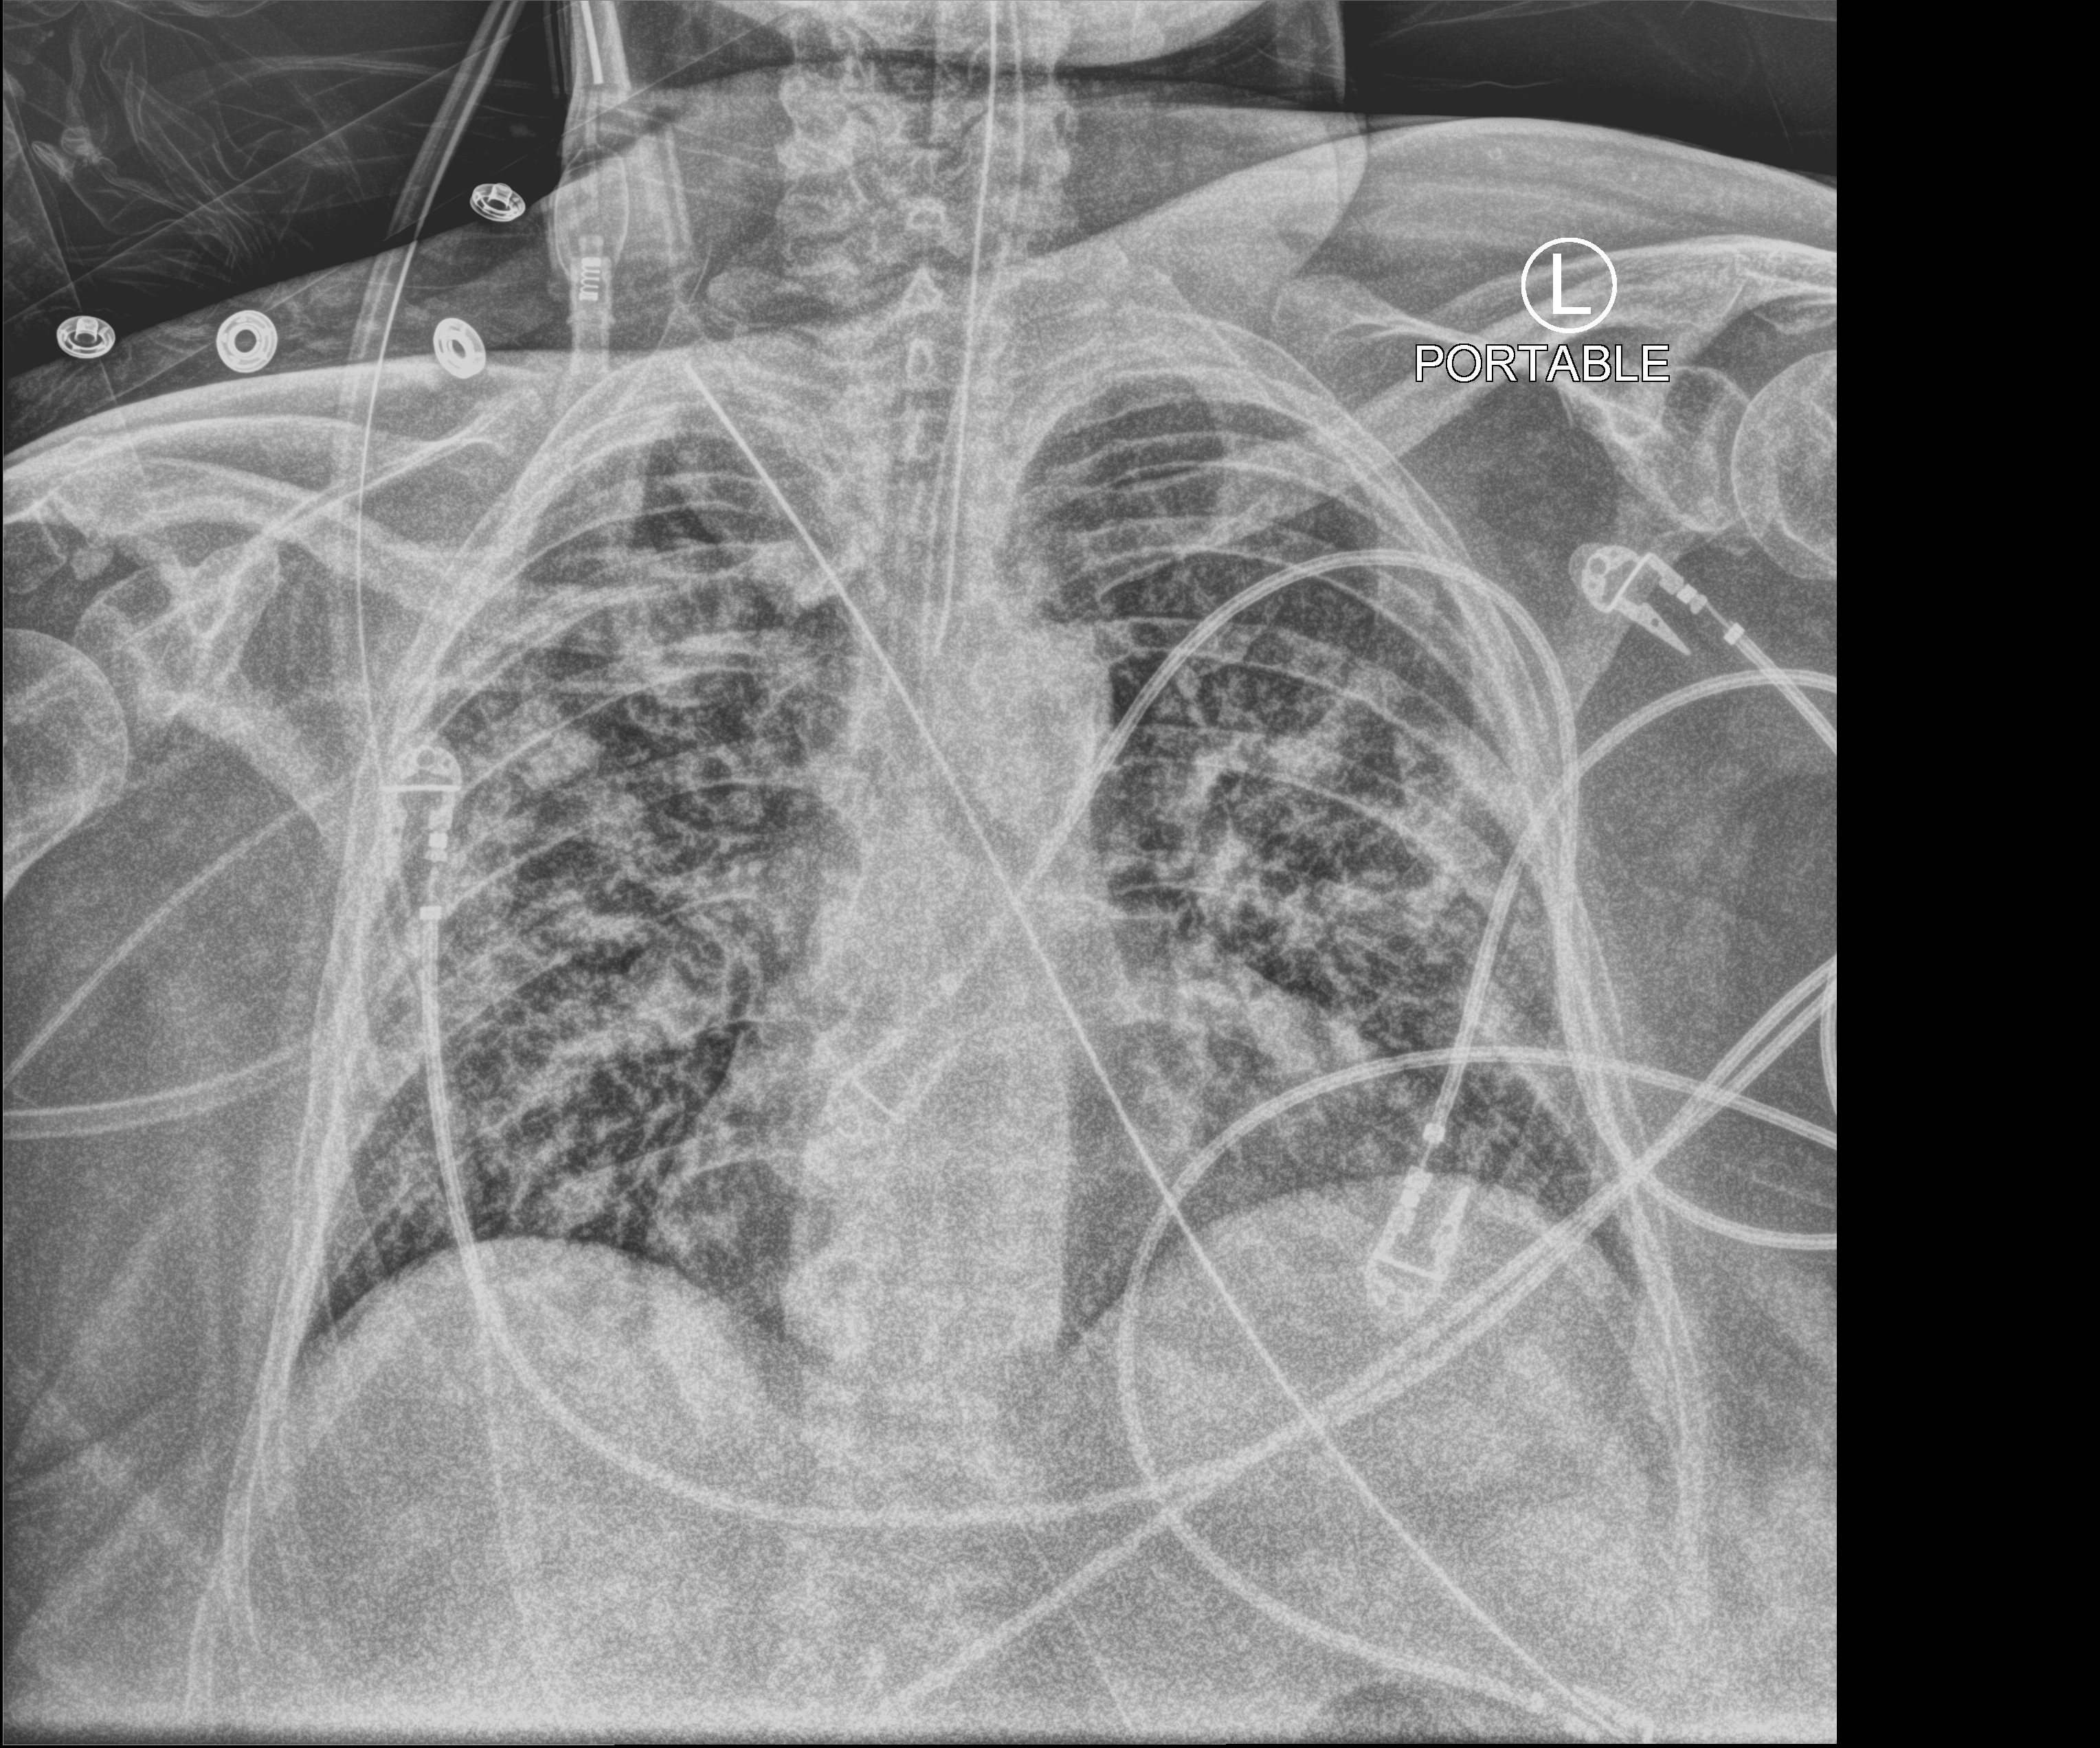
Portable chest radiograph; anteroposterior (AP) projection. Female patient hospitalised with COVID-19, age 75–90 years.
From the hospital-stay record, not from the radiograph (when in the stay this image was taken is not recorded): admitted to intensive care during this hospital stay: yes; smoking status (admission record): former.